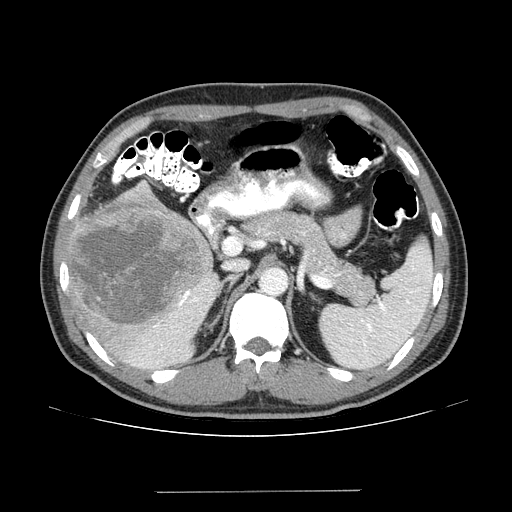
Contrast-enhanced abdominal CT (liver protocol), one axial slice; position 82 of 131 along the scan axis; reconstruction kernel STANDARD; 100 kVp; one of 2 acquisitions stored at this slice position; soft-tissue window (W 400 / L 40 HU); 2.5 mm slice thickness; 512 × 512 image matrix, field of view 380 × 380 mm. From the clinical record (not read from this slice): diagnosis: hepatocellular carcinoma (patient treated with transarterial chemoembolisation; whether this scan precedes or follows treatment is not stated here); TNM stage (as recorded): Stage-I.
Annotated regions visible in this slice (semi-automatic segmentation, software-assisted and operator-edited):
- liver parenchyma outside the tumour (the mass and vessels are separate outlines, so this box may not span the whole liver): bounding box (x1, y1, x2, y2) in pixels: (66, 182, 220, 370)
- mass: (68, 188, 211, 331)
- liver vessels: (139, 290, 208, 366)